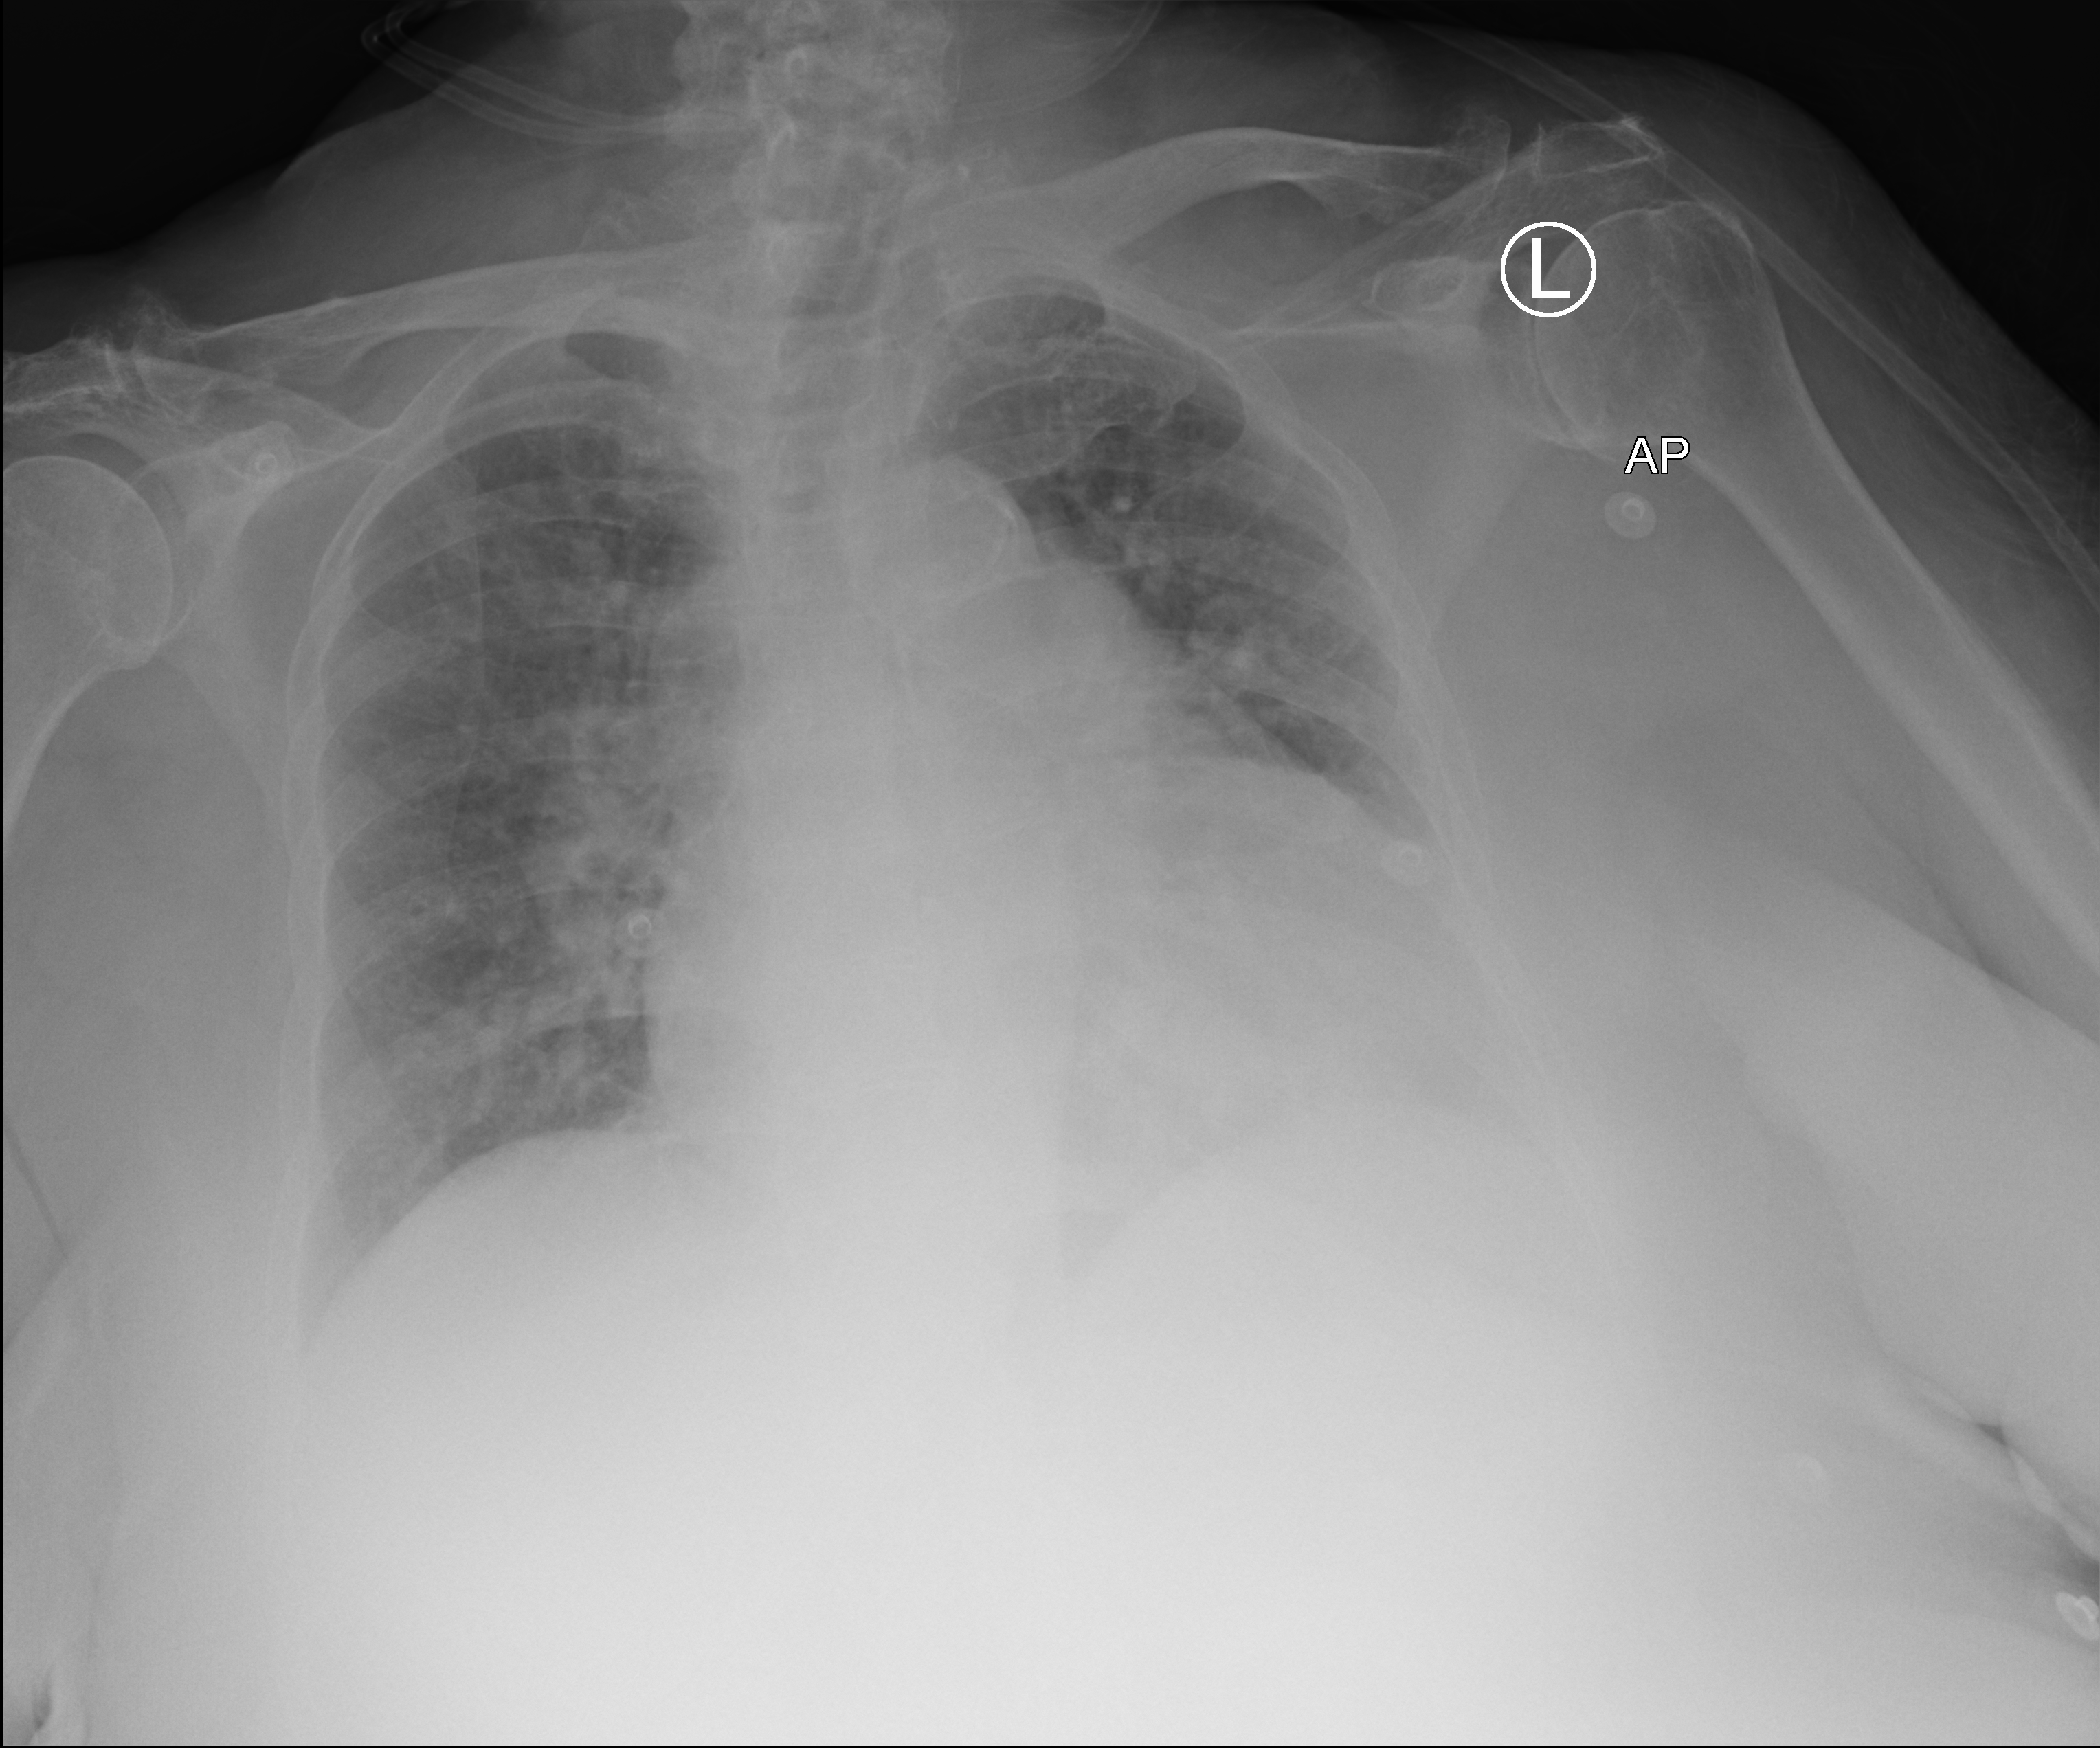
Bedside chest radiograph (computed radiography). Patient hospitalised with COVID-19; female, aged 75–90 years.
Hospital-stay facts (about this admission, not read from this image; timing relative to this image not recorded): other chronic lung disease (admission record): no.